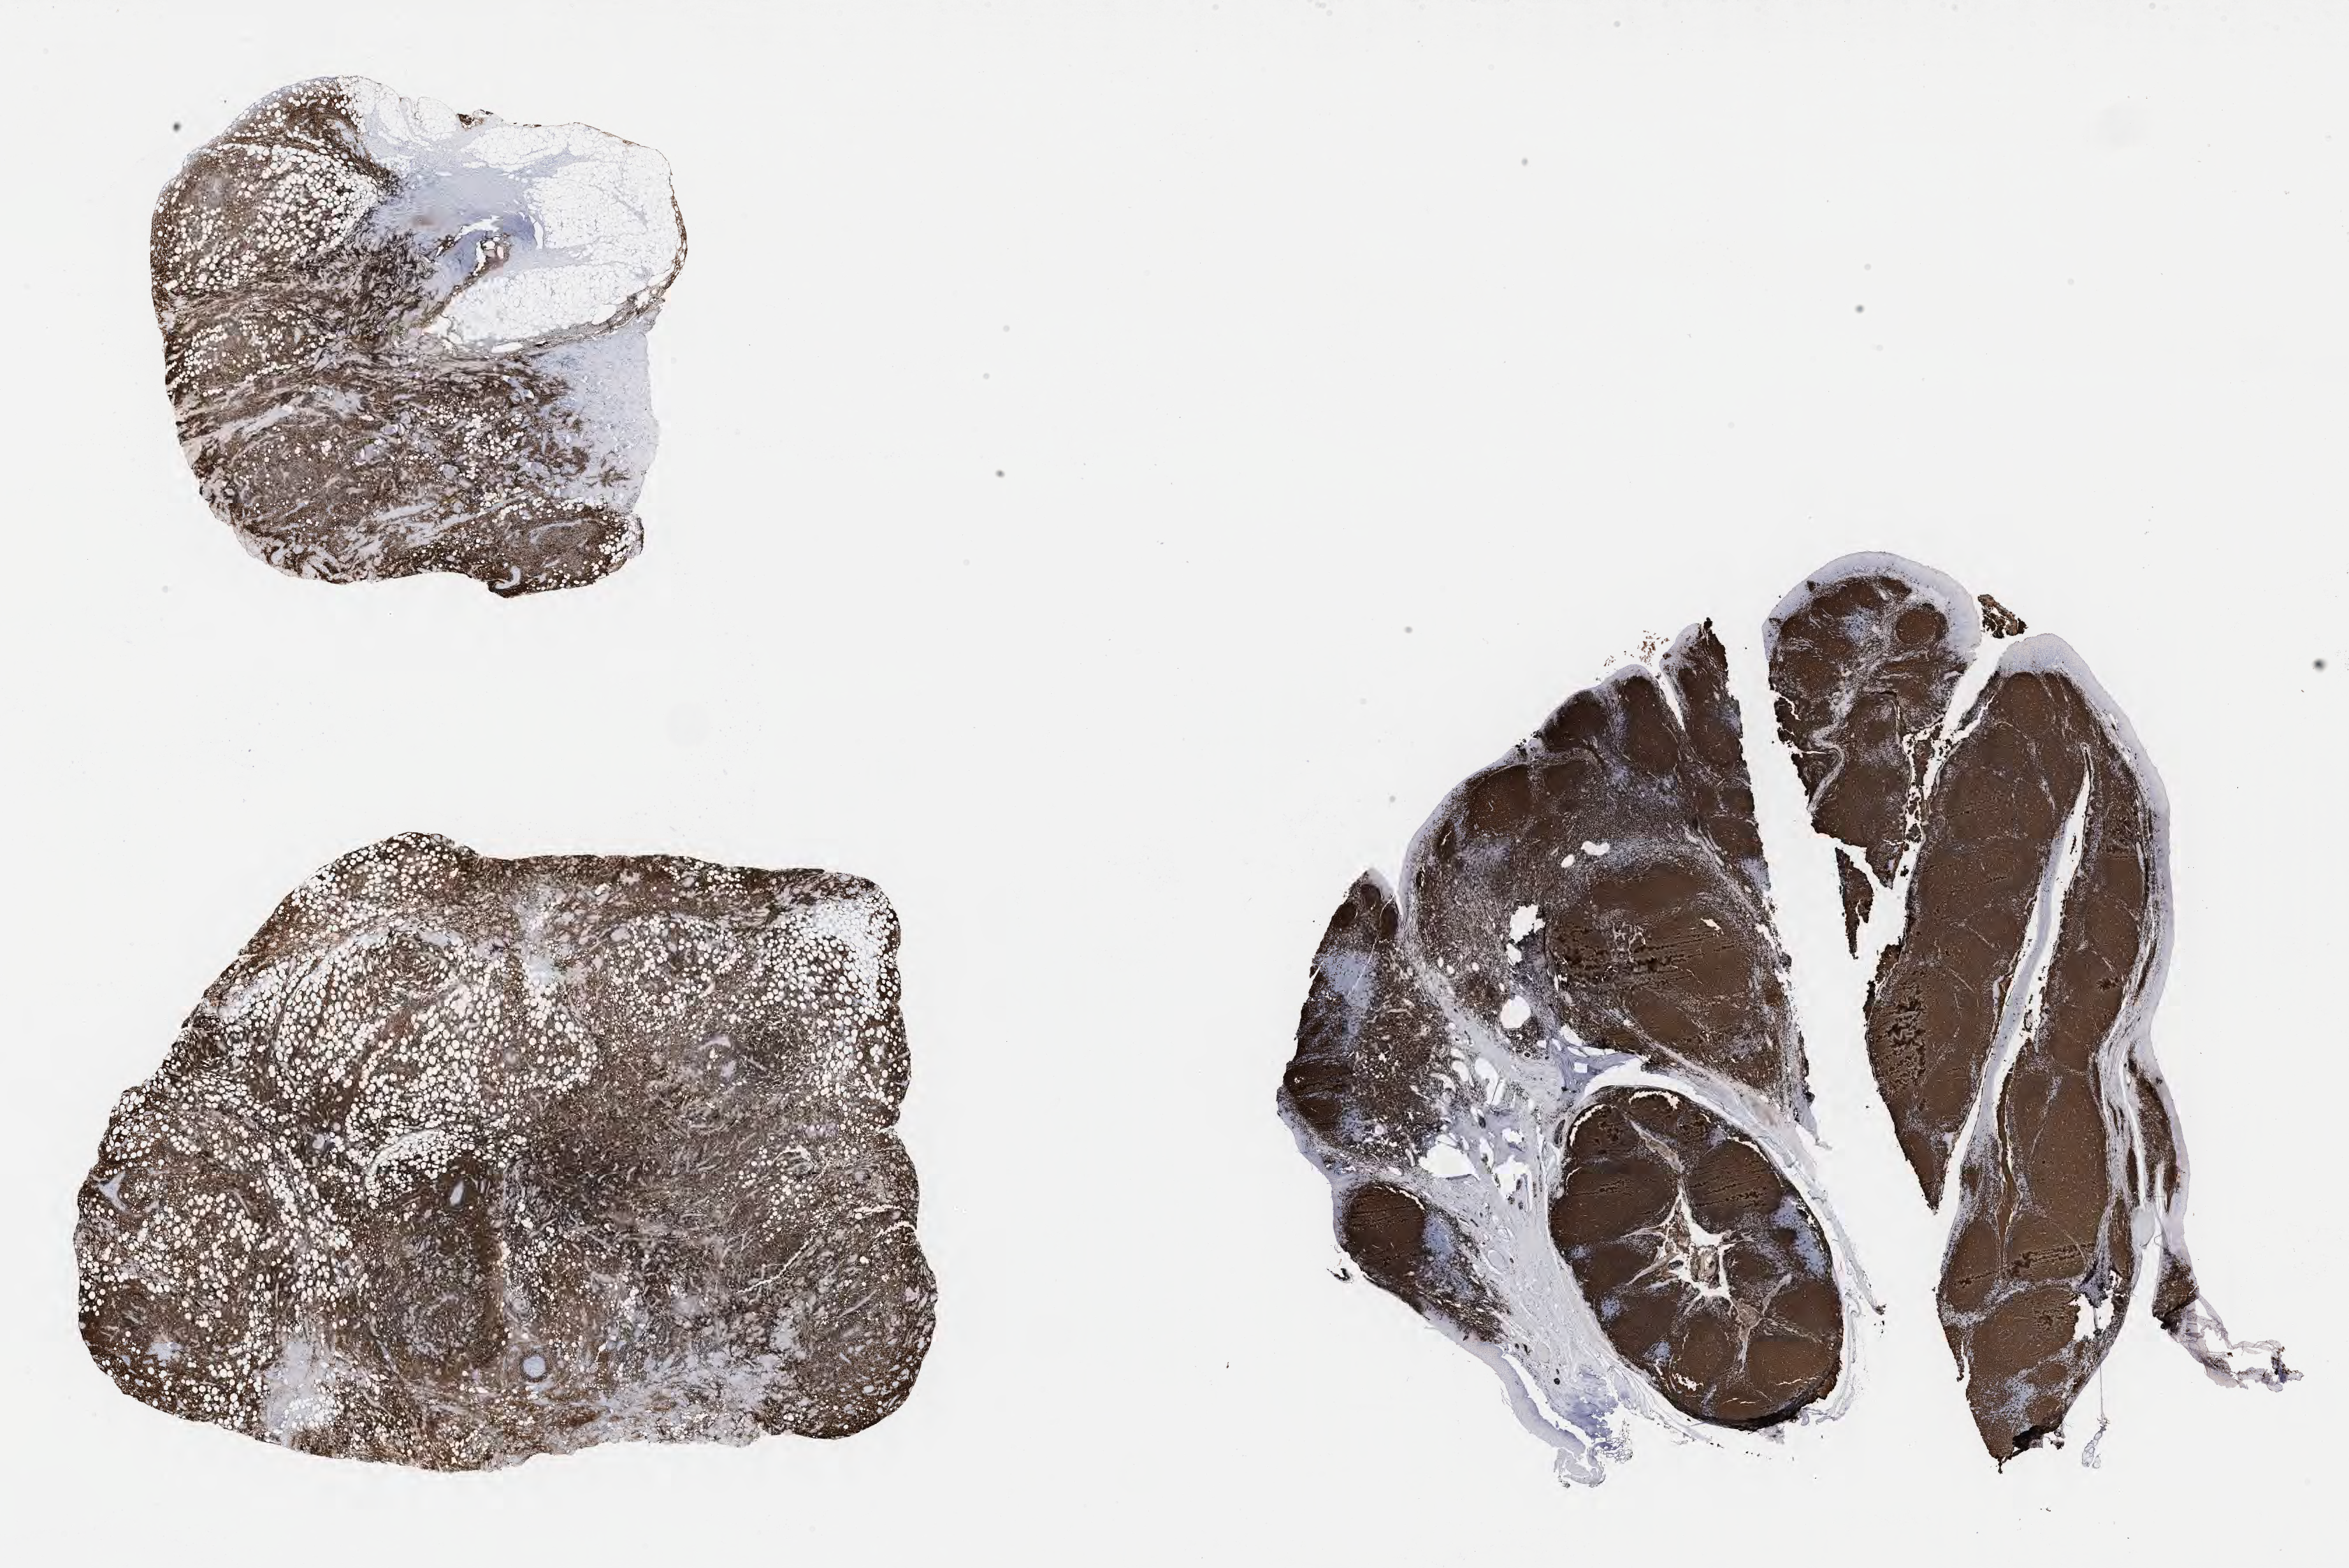
Whole-slide image, immunohistochemical stain for CD20, low-resolution overview of the scanned area, about 27.2 x 18.1 mm. Specimen: tumor tissue. Site: kidney. Male patient, 63 years old.
Diagnosis: Diffuse large B-cell lymphoma, NOS.